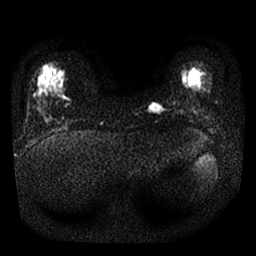
Breast MRI, one axial slice. Position 3 of 24 along the scan axis. Diffusion-weighted series; image 2 of 4 stored at this slice position (different b-values; order by instance number). 1.5 T. 4 mm slice thickness. 256 × 256 image matrix. Female patient.
Annotated regions visible in this slice (manually delineated by an expert):
- tumour on diffusion-weighted imaging: bounding box <150,104,162,112> (left, top, right, bottom; pixels)